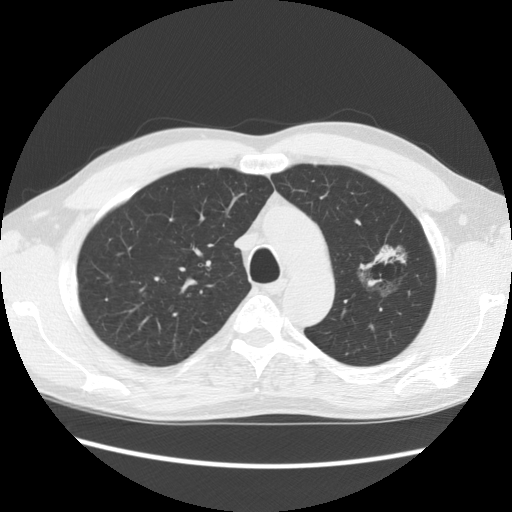
Chest CT (low-dose screening protocol), one axial image. Second screening round (one year after baseline). Lung window (W 1500 / L -600 HU). 2.5 mm slice thickness. Standard (soft-tissue) reconstruction kernel (STANDARD). 140 kVp. Slice 103 of 139 in the series. 512 × 512 image matrix, field of view 360 × 360 mm. Male, age 61 years at enrolment.
- Expert reader's lesion annotation, bounding box <345,224,424,300> (left, top, right, bottom; pixels).
- Reader record for this screening exam (exam-level; its link to the box is not recorded): non-calcified nodule or mass ≥4 mm, left upper lobe, 34 × 32 mm, poorly defined margins, mixed attenuation, pre-existing on the prior screen: yes; interval growth: no.
- Official screen result: positive, no significant change: stable abnormalities potentially related to lung cancer, unchanged since the prior screening exam.